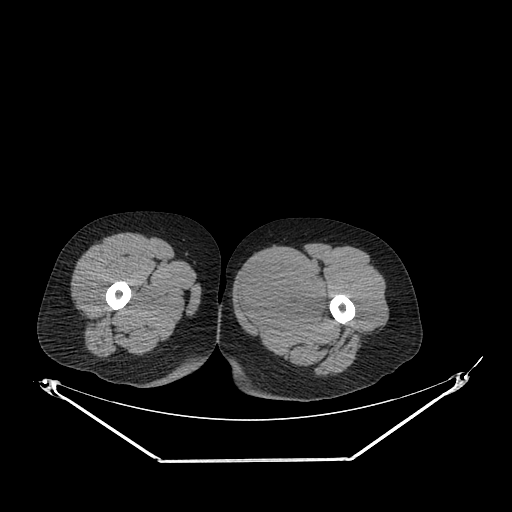
CT of an extremity soft-tissue mass (from a PET/CT study), one axial slice; position 239 of 267 along the scan axis; soft-tissue window (W 400 / L 40 HU); 512 × 512 image matrix, field of view 500 × 500 mm. Female patient. From the clinical record (not read from this slice): histological type: pleiomorphic leiomyosarcoma; grade: intermediate; site of the primary tumour: left thigh.
Outlined on this slice (expert contour drawn on MRI and transferred to this co-registered scan by the dataset authors):
- gross tumour volume including surrounding oedema: bounding box [x1, y1, x2, y2] px = [237, 258, 328, 332]
- gross tumour volume (mass): [237, 258, 325, 330]